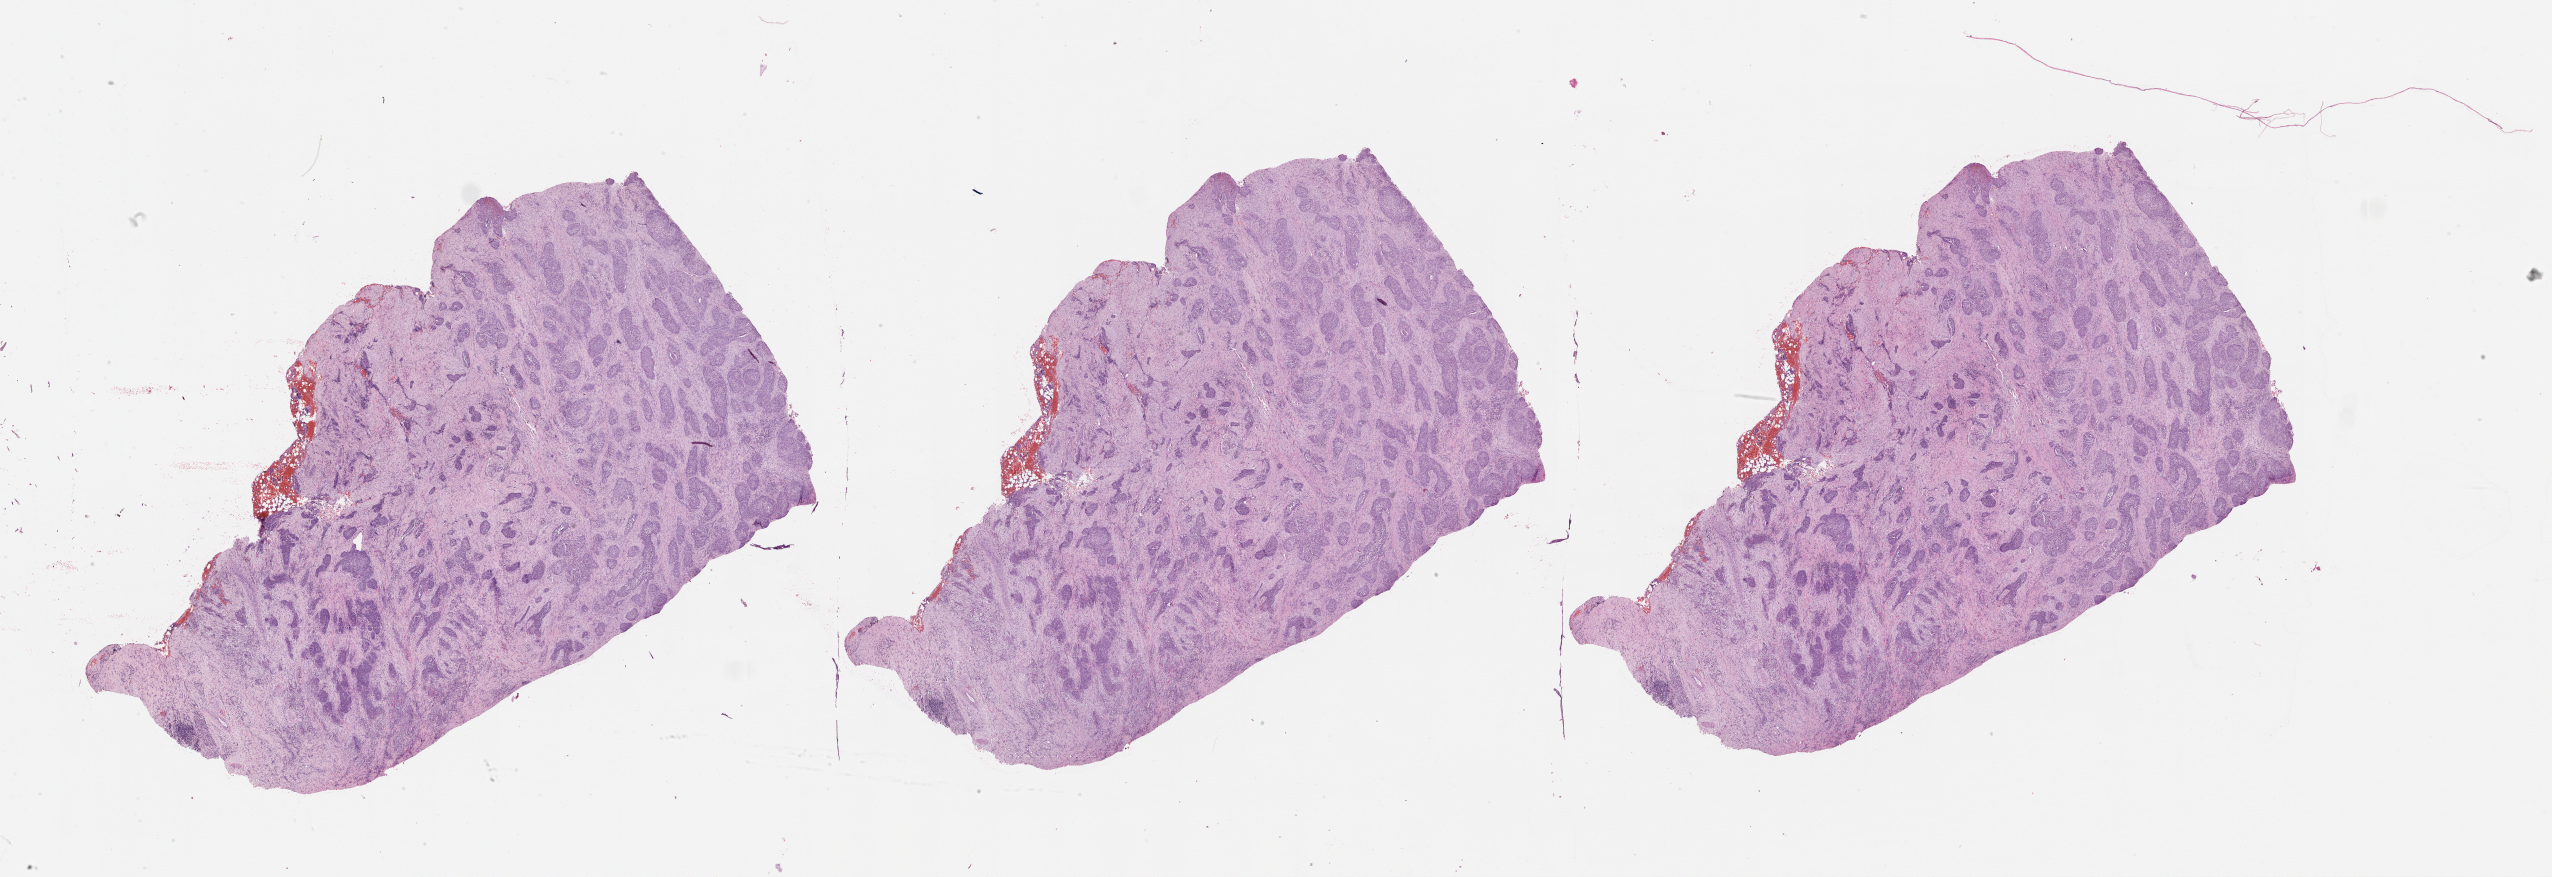
Hematoxylin and eosin (H&E) stained whole-slide image — low-resolution overview of the scanned area, about 41.1 x 14.1 mm (acquisition: 20x scan), tumour tissue sample, lung. Male, 74 y/o.
- patient diagnosis (cohort enrolment): squamous cell carcinoma (lung)